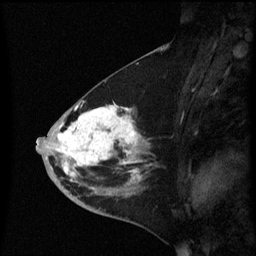
Breast MRI (dynamic contrast-enhanced), one sagittal slice; position 28 of 60 along the scan axis; dynamic contrast-enhanced series, image 2 of 3 at this slice position (ordered by acquisition); 1.5 T; TE 4.2 ms, TR 8.4 ms; 2.3 mm slice thickness; 256 × 256 image matrix. Female patient, age 46 years. Case-level facts recorded for this patient, not image findings: setting: breast cancer imaged before/during neoadjuvant chemotherapy; receptor status: HER2-positive.
Structures marked on this image (semi-automatic segmentation, software-assisted and operator-edited):
- analysis volume of interest (the breast-tissue region the enhancement analysis was run in; not a lesion): bounding box (x1, y1, x2, y2) in pixels: (36, 96, 150, 187)
- tumour enhancement mask (voxels above the 70 % enhancement threshold inside the analysis volume of interest): (37, 104, 141, 181)